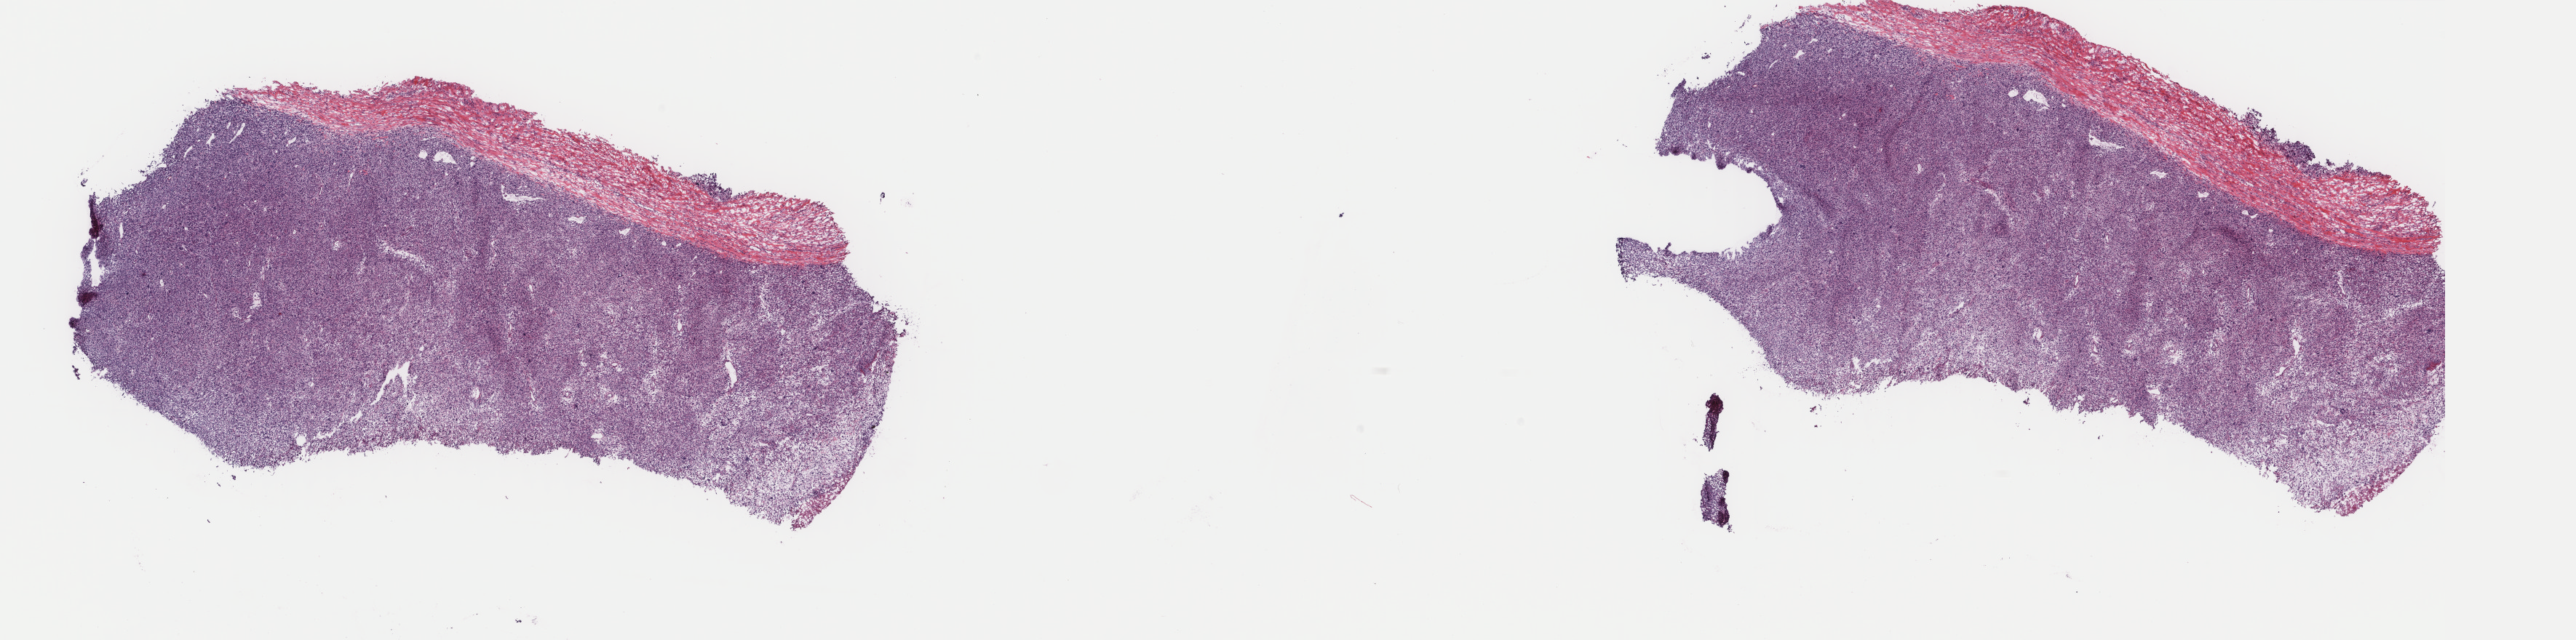
Digitized H&E tissue section (whole slide) — shown as a low-resolution overview of the whole scanned area (about 28.1 x 7.0 mm, slide scanned at 40x), frozen section, primary tumour sample from the connective, subcutaneous and other soft tissues. Patient: male, age at initial diagnosis 47 years. Slide review estimates, as recorded: tumour cells 90%, tumour nuclei 93%, normal cells 0%, stromal cells 10%, necrosis 0%. Inflammatory infiltration, as recorded: lymphocyte infiltration 0%, monocyte infiltration 0%, neutrophil infiltration 0%.
Diagnosis: Undifferentiated sarcoma.